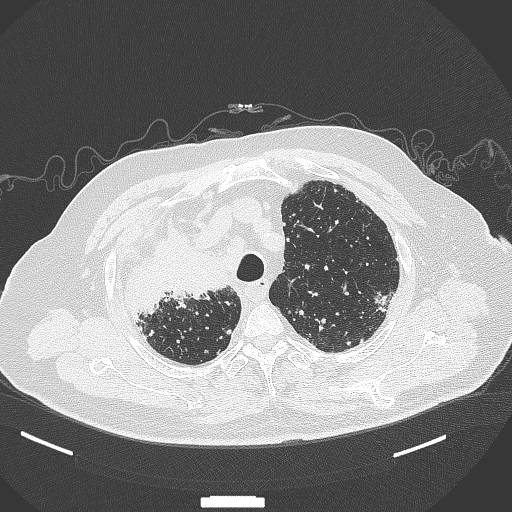
Chest CT, one axial slice; position 291 of 384 along the scan axis; lung window (W 1500 / L -600 HU); 512 × 512 image matrix, field of view 400 × 400 mm. Male patient, age 69 years. From the clinical record (not read from this slice): clinical TNM (as recorded): T4 N3 M1.
Structures marked on this image (rectangle marked by the reading radiologist):
- lung tumour (recorded histology: adenocarcinoma): bounding box (x1, y1, x2, y2) in pixels: (123, 212, 230, 325)